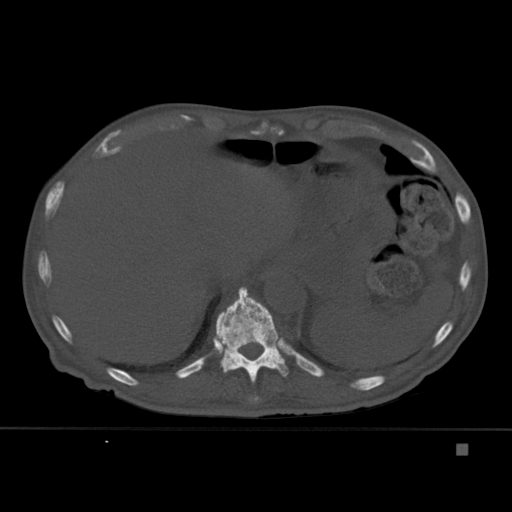
CT including the spine, one axial slice; slice 218 of 451 in the series (ordered by position); bone window (W 1800 / L 400 HU); 512 × 512 image matrix, field of view 378 × 378 mm. Patient: male, 75 years. From the clinical record (not read from this slice): primary cancer: prostate.
Outlined on this slice (semi-automatic segmentation, software-assisted and operator-edited):
- T10 vertebra: bounding box (x1, y1, x2, y2) in pixels: (251, 377, 259, 404)
- T11 vertebra: (213, 287, 289, 383)